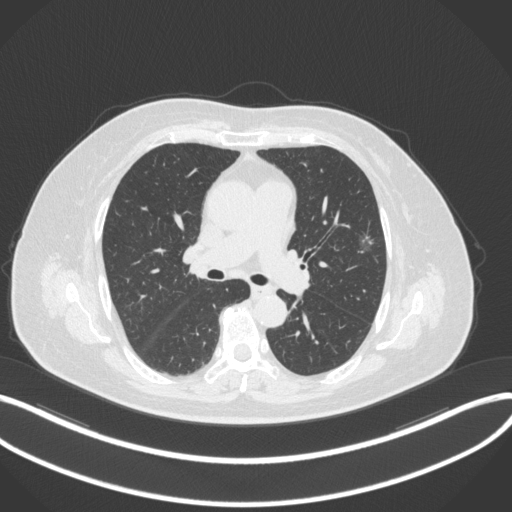
Chest CT, one axial slice; position 186 of 286 along the scan axis; reconstruction kernel B31f; 120 kVp; lung window (W 1500 / L -600 HU); 1 mm slice thickness; 512 × 512 image matrix, field of view 400 × 400 mm. Patient: female, 76 years. From the clinical record (not read from this slice): clinical TNM (as recorded): T1b N0 M0.
Structures marked on this image (rectangle marked by the reading radiologist):
- lung tumour (recorded histology: adenocarcinoma): bounding box (x1, y1, x2, y2) in pixels: (350, 225, 383, 257)